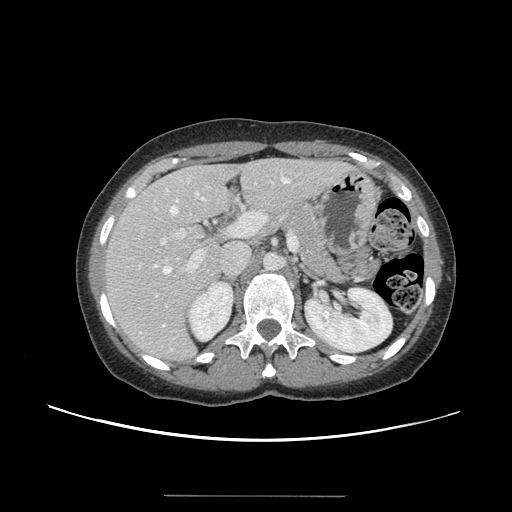
Contrast-enhanced abdominal CT, one axial slice. Slice 82 of 144 in the series (ordered by position). 120 kVp. Intravenous contrast given. Soft-tissue window (W 400 / L 40 HU). 2.5 mm slice thickness. 512 × 512 image matrix, field of view 380 × 380 mm. Female patient, age 53 years. Case-level facts recorded for this patient, not image findings: diagnosis: colorectal cancer liver metastases, imaged before liver resection; multiple liver metastases: yes; largest metastasis: 1.1 cm; disease in both lobes: no.
Outlined on this slice (expert manual segmentation):
- hepatic veins: box from (x=163, y=178) to (x=290, y=326) px
- liver: (x=107, y=160)–(x=346, y=361)
- planned liver remnant (the part of the liver to remain after resection): (x=107, y=159)–(x=315, y=298)
- portal vein (with intrahepatic branches): (x=139, y=207)–(x=298, y=297)